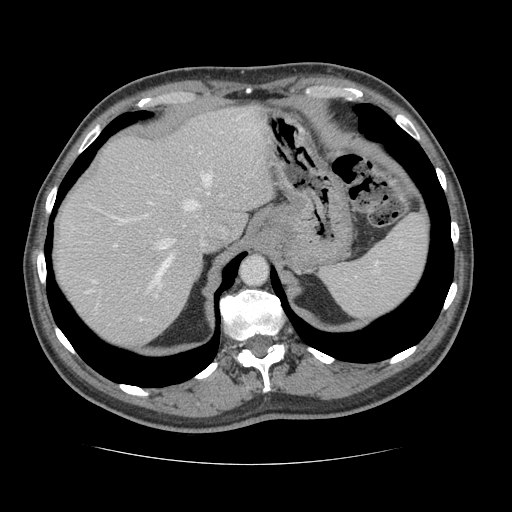
Contrast-enhanced abdominal CT, one axial slice. Slice 101 of 134 in the series (ordered by position). Reconstruction kernel STANDARD. 120 kVp. Intravenous contrast given. Soft-tissue window (W 400 / L 40 HU). 2.5 mm slice thickness. 512 × 512 image matrix, field of view 377 × 377 mm. Male patient, age 68 years. Case-level facts recorded for this patient, not image findings: diagnosis: colorectal cancer liver metastases, imaged before liver resection; multiple liver metastases: yes; largest metastasis: 2.2 cm.
Structures marked on this image (expert manual segmentation):
- hepatic veins: bounding box <87,174,211,320> (left, top, right, bottom; pixels)
- liver: <53,106,273,350>
- planned liver remnant (the part of the liver to remain after resection): <53,106,273,324>
- portal vein (with intrahepatic branches): <114,244,157,297>